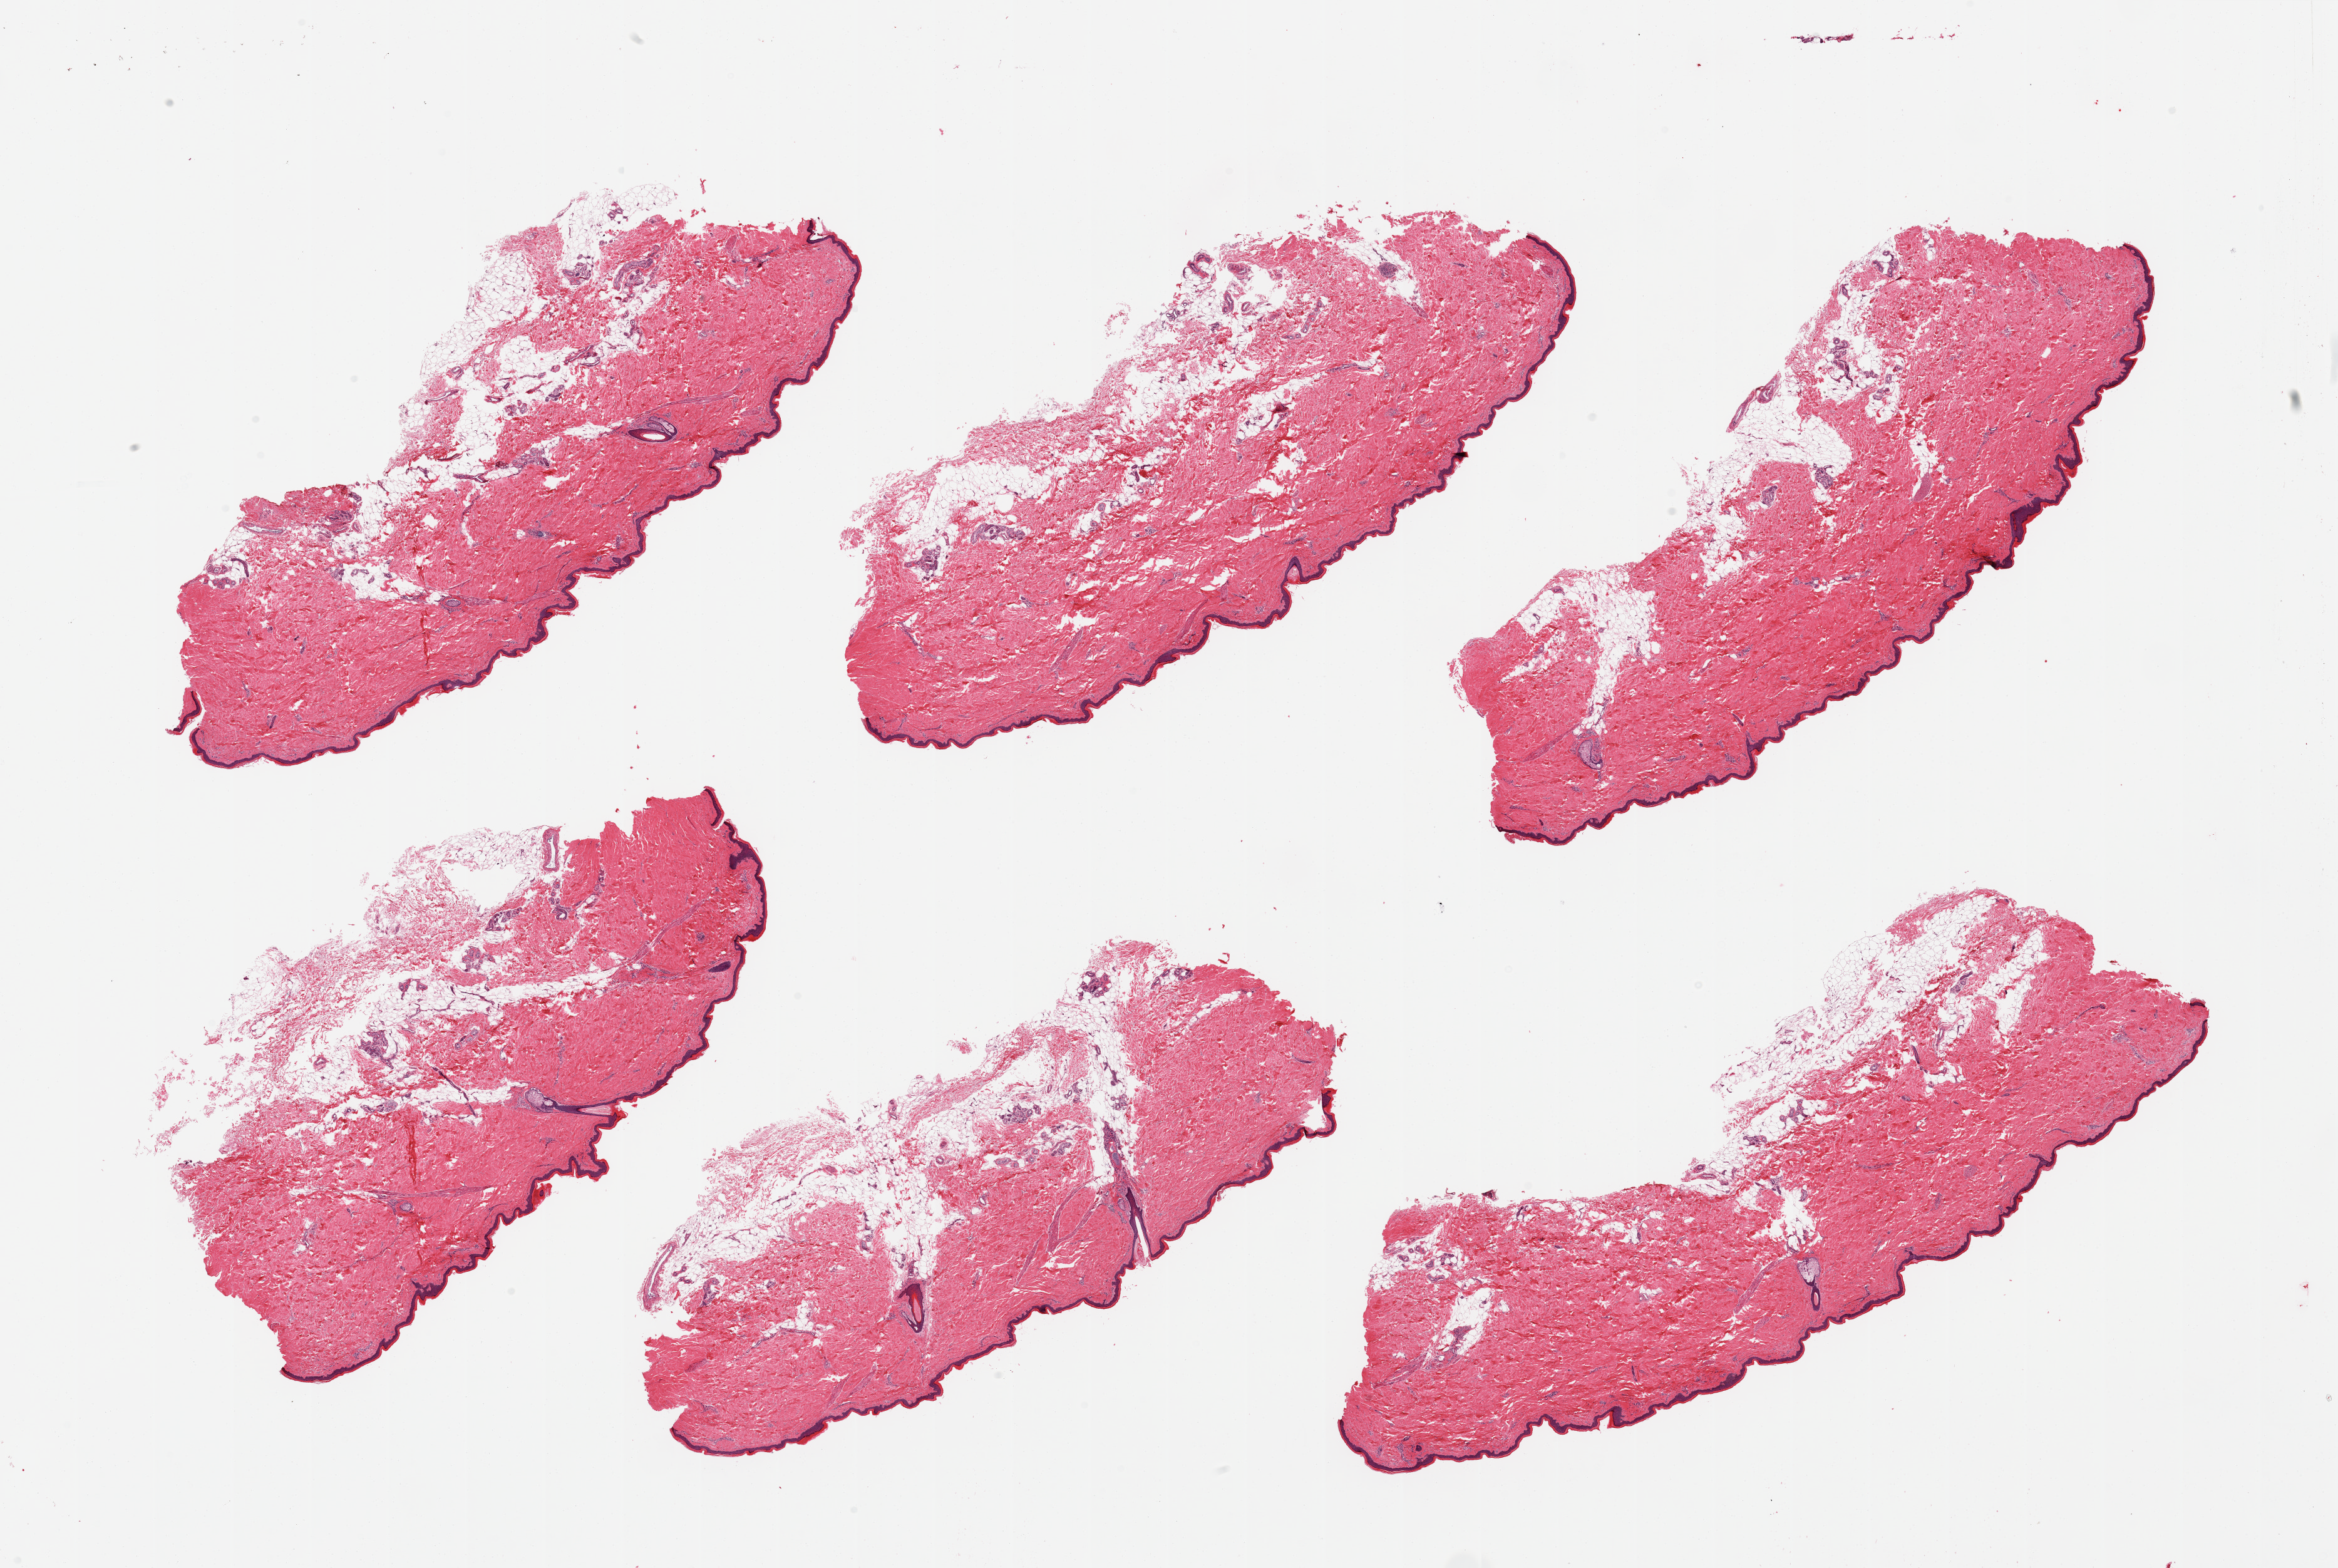
Digitized hematoxylin and eosin (H&E)-stained section, brightfield, shown as a low-resolution overview of the whole scanned area (about 29.5 x 19.8 mm), PAXgene-fixed, paraffin-embedded tissue, section of skin of lower leg (target tissue), tissue donor sample. Donor sex: male.
- reviewer comment on this tissue sample: 6 pieces; considerable deep fat and intradermal fat